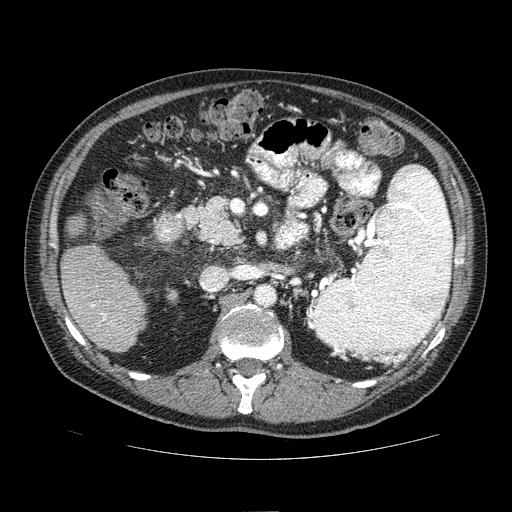
Contrast-enhanced abdominal CT (liver protocol), one axial slice. 100 kVp. One of 2 acquisitions stored at this slice position. Soft-tissue window (W 400 / L 40 HU). 2.5 mm slice thickness. 512 × 512 image matrix. Case-level facts recorded for this patient, not image findings: diagnosis: hepatocellular carcinoma (patient treated with transarterial chemoembolisation; whether this scan precedes or follows treatment is not stated here); TNM stage (as recorded): Stage-IIIA; Child-Pugh class: A; tumour nodularity: multinodular; tumour size: 5.6 cm.
Annotated regions visible in this slice (semi-automatically segmented with operator editing):
- liver parenchyma outside the tumour (the mass and vessels are separate outlines, so this box may not span the whole liver): bounding box <60,216,146,352> (left, top, right, bottom; pixels)
- liver vessels: <90,301,127,331>